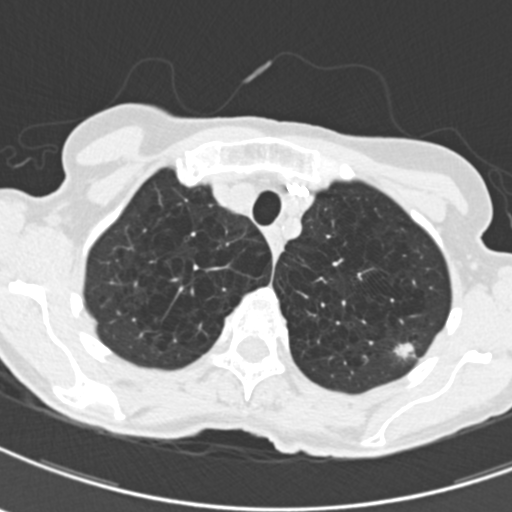
Axial slice from a low-dose chest CT screening exam; third annual screen; lung window (W 1500 / L -600 HU); slice 38 of 203 in the series; 512 × 512 image matrix. Female participant, aged 71 years at enrolment. Current smoker at enrolment.
• Lesion marked by an expert reader, bounding box (x1, y1, x2, y2) in pixels: (386, 331, 428, 371).
• Screening reader's record for this exam (one nodule recorded; not confirmed to be the boxed lesion): non-calcified nodule or mass ≥4 mm, left upper lobe, 12 × 9 mm, spiculated (stellate) margins, mixed attenuation, pre-existing on the prior screen: yes; interval growth: yes.
• Official screen result: positive, other.
• Lung cancer was diagnosed 114 days after this screen: adenocarcinoma, NOS, left upper lobe, moderately differentiated (G2), stage IA (AJCC 6th edition), 12 mm at pathology.